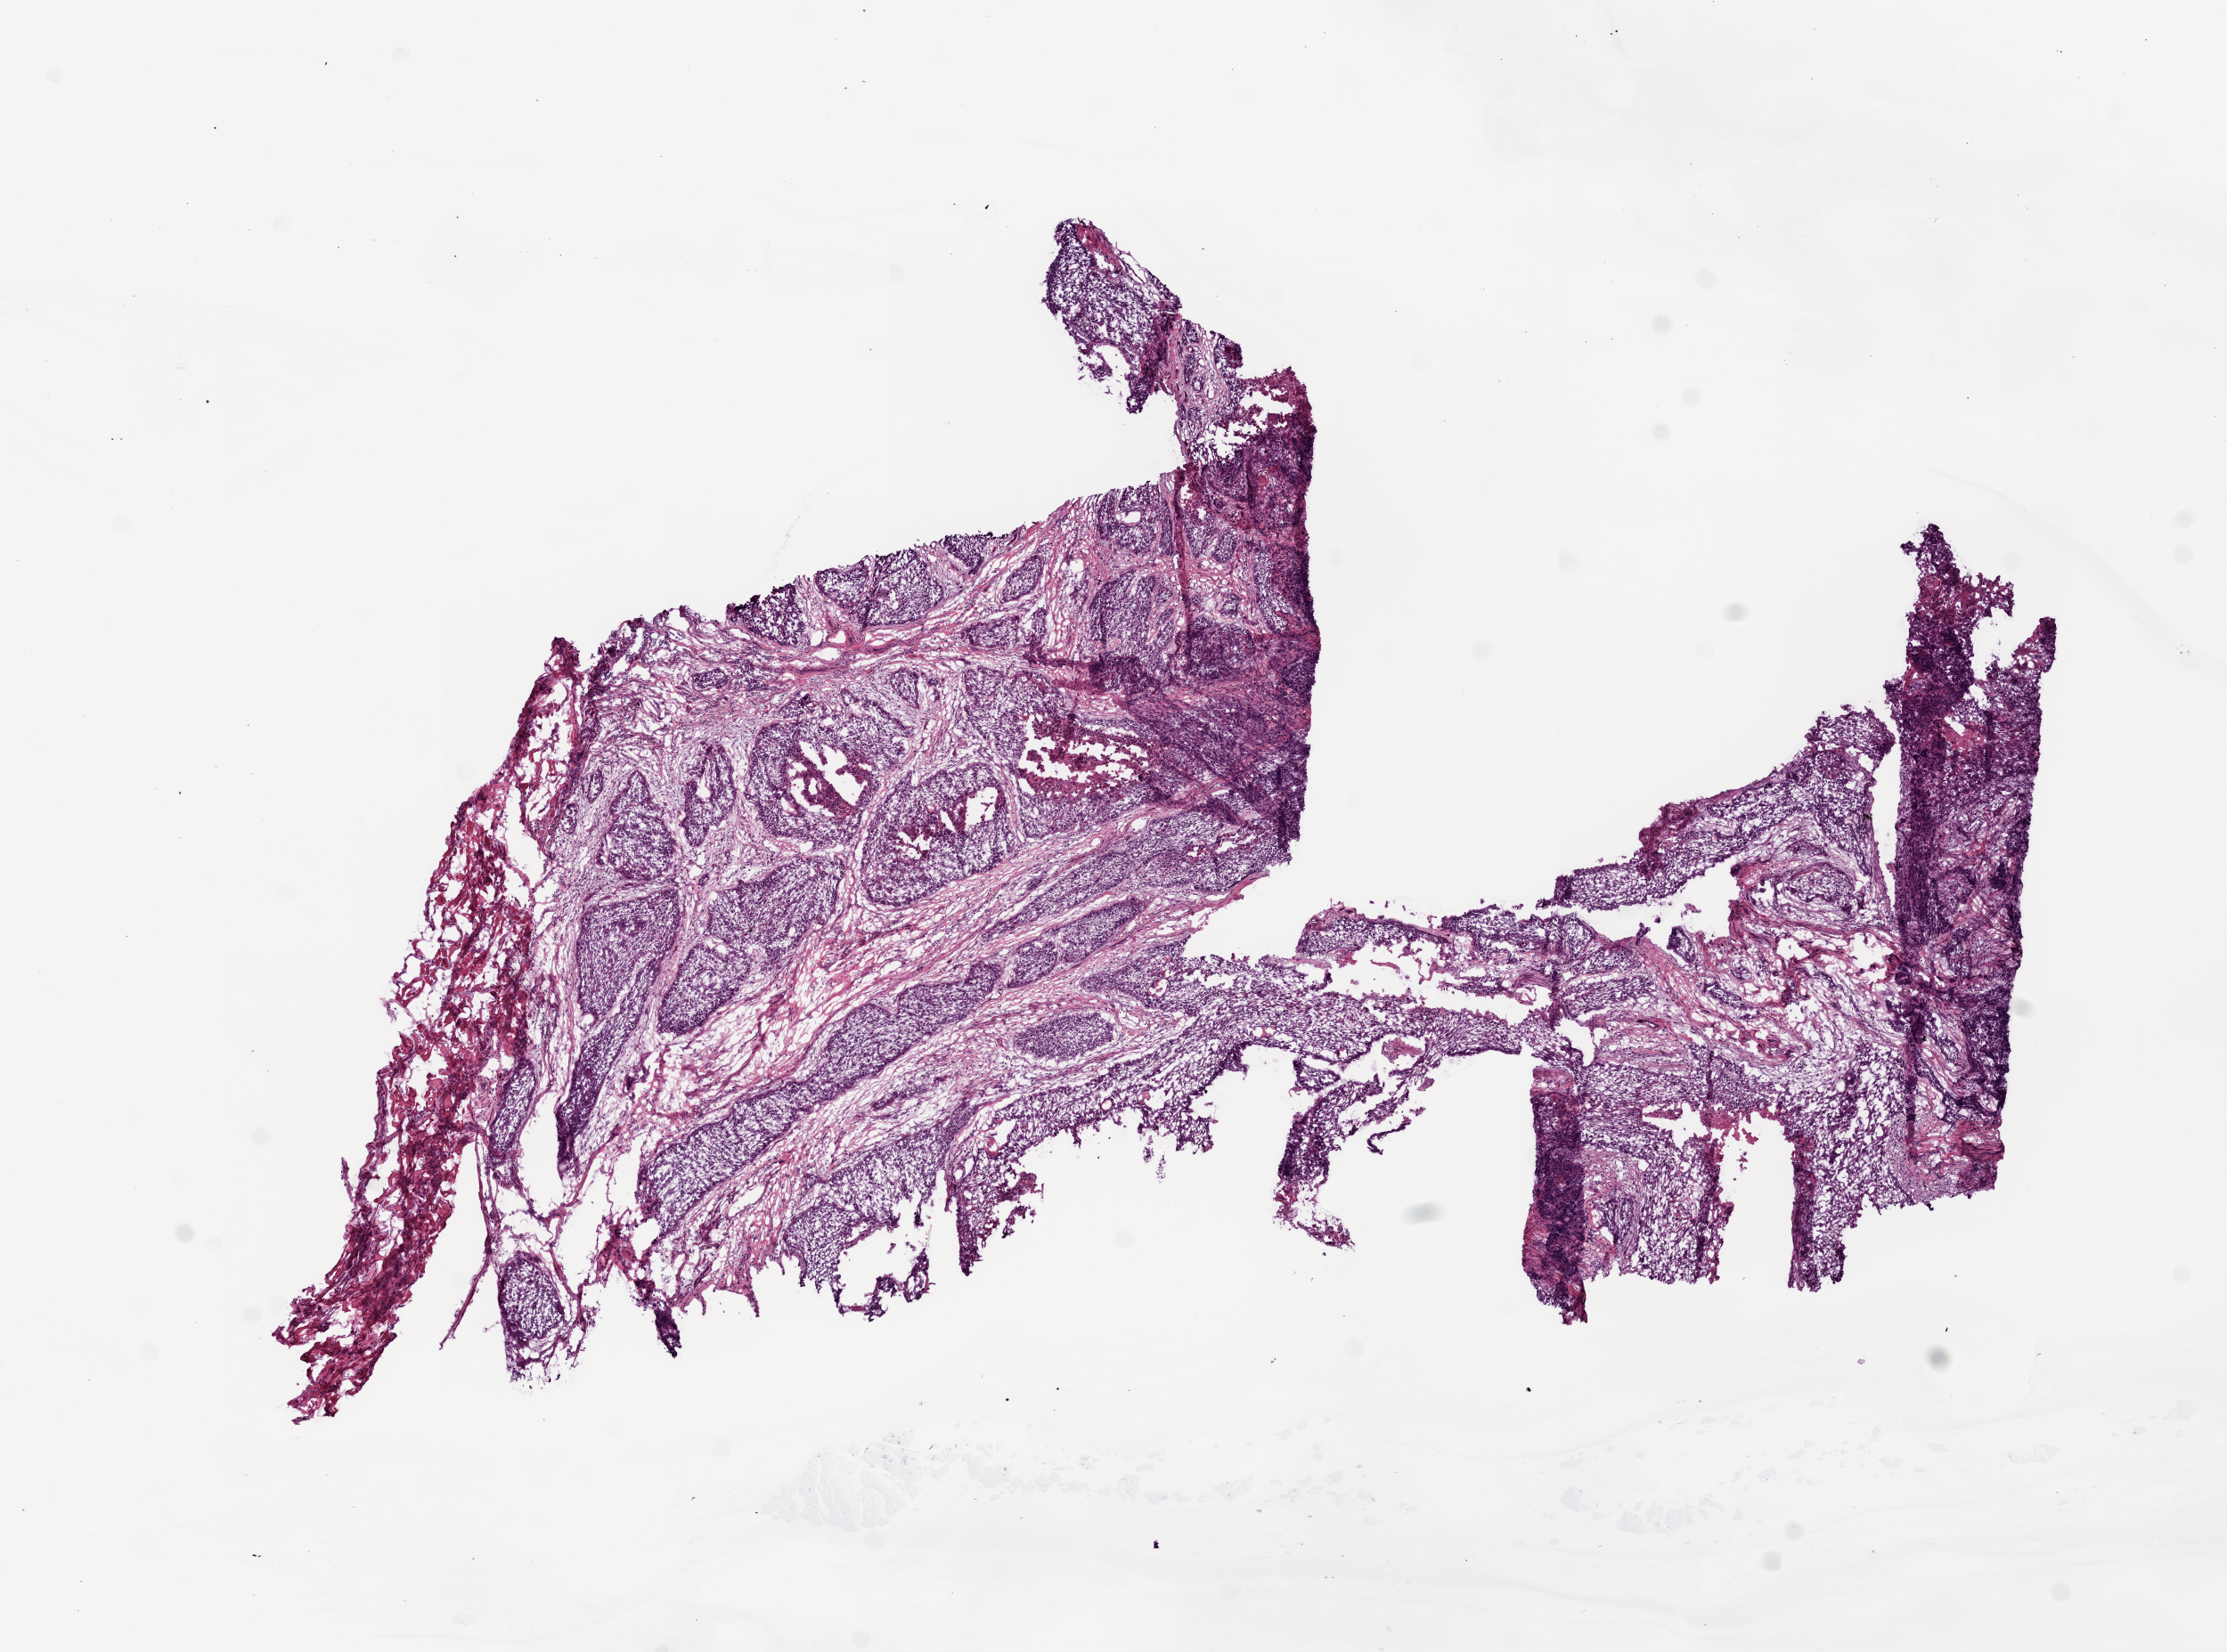
Digitized H&E tissue section (whole slide), low-resolution overview of the scanned area, about 10.0 x 7.4 mm. Frozen section from the top of the tissue portion. Head and neck, primary tumour sample. Male patient; age at initial diagnosis 57 years. Histologic grade: G3 (poorly differentiated). Composition of this section per pathologist review: tumour cells 70%, tumour nuclei 75%, normal cells 0%, stromal cells 30%, necrosis 0%.
AJCC pathologic stage: IVA (7th edition). Histologic diagnosis: Squamous cell carcinoma, NOS (larynx, NOS).